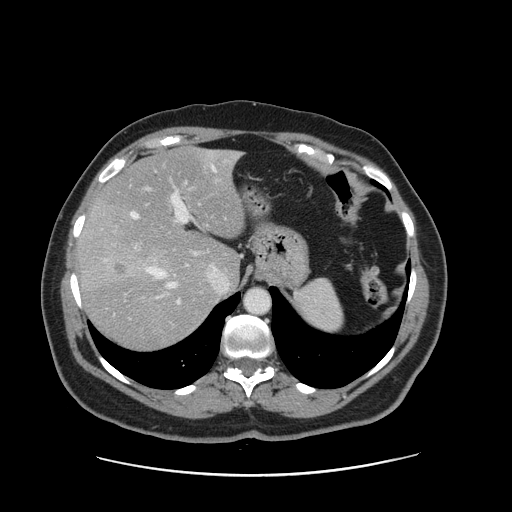
Contrast-enhanced abdominal CT, one axial slice; position 112 of 161 along the scan axis; intravenous contrast given; soft-tissue window (W 400 / L 40 HU); 2.5 mm slice thickness; 512 × 512 image matrix, field of view 398 × 398 mm. Female patient, age 62 years. Case-level facts recorded for this patient, not image findings: diagnosis: colorectal cancer liver metastases, imaged before liver resection; multiple liver metastases: no; largest metastasis: 2.5 cm; disease in both lobes: no.
Annotated regions visible in this slice (expert manual segmentation):
- hepatic veins: bounding box <131,154,239,291> (left, top, right, bottom; pixels)
- liver: <80,148,245,351>
- planned liver remnant (the part of the liver to remain after resection): <97,148,245,281>
- portal vein (with intrahepatic branches): <125,181,193,304>
- liver metastasis: <115,263,126,275>